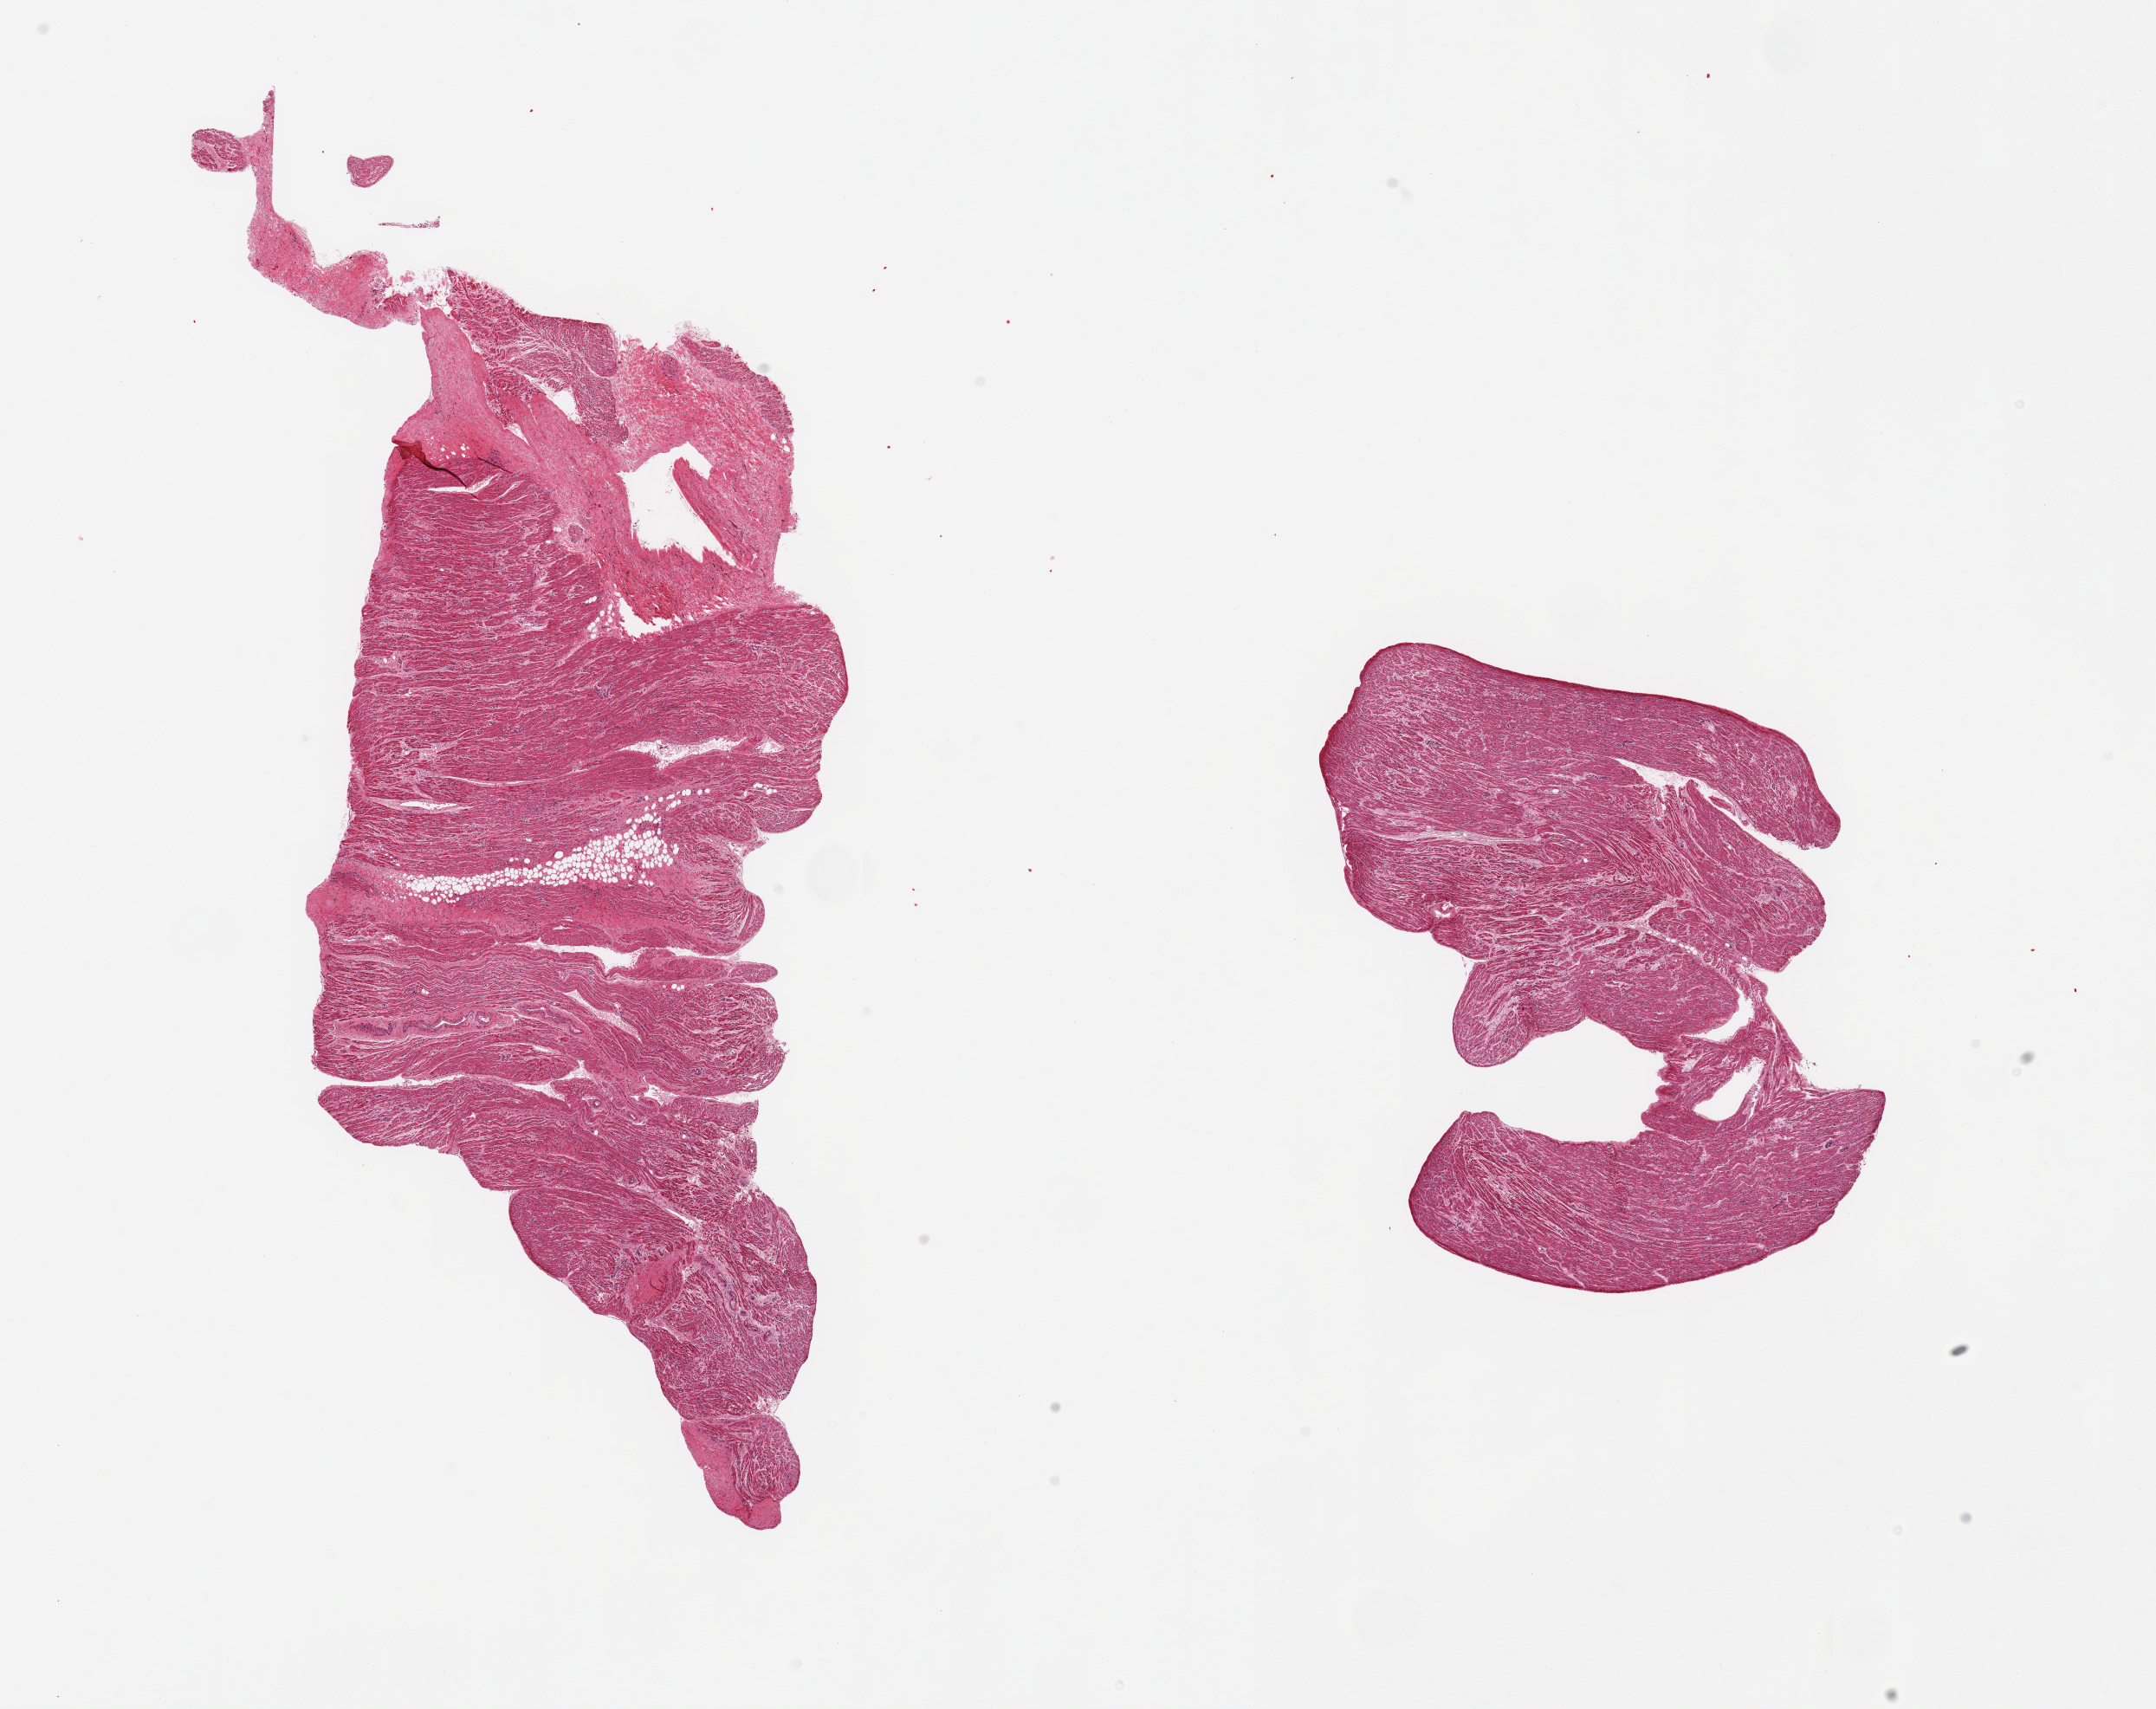
Digitized haematoxylin and eosin-stained section, low-resolution overview of the scanned area, about 19.7 x 15.6 mm. PAXgene-fixed, paraffin-embedded tissue. Target tissue: auricular appendage. Tissue donor sample. Donor: male.
• reviewer comment on this tissue sample: 2 pieces; 20% internal fibrofatty tissue in 1 piece; otherwise well dissected